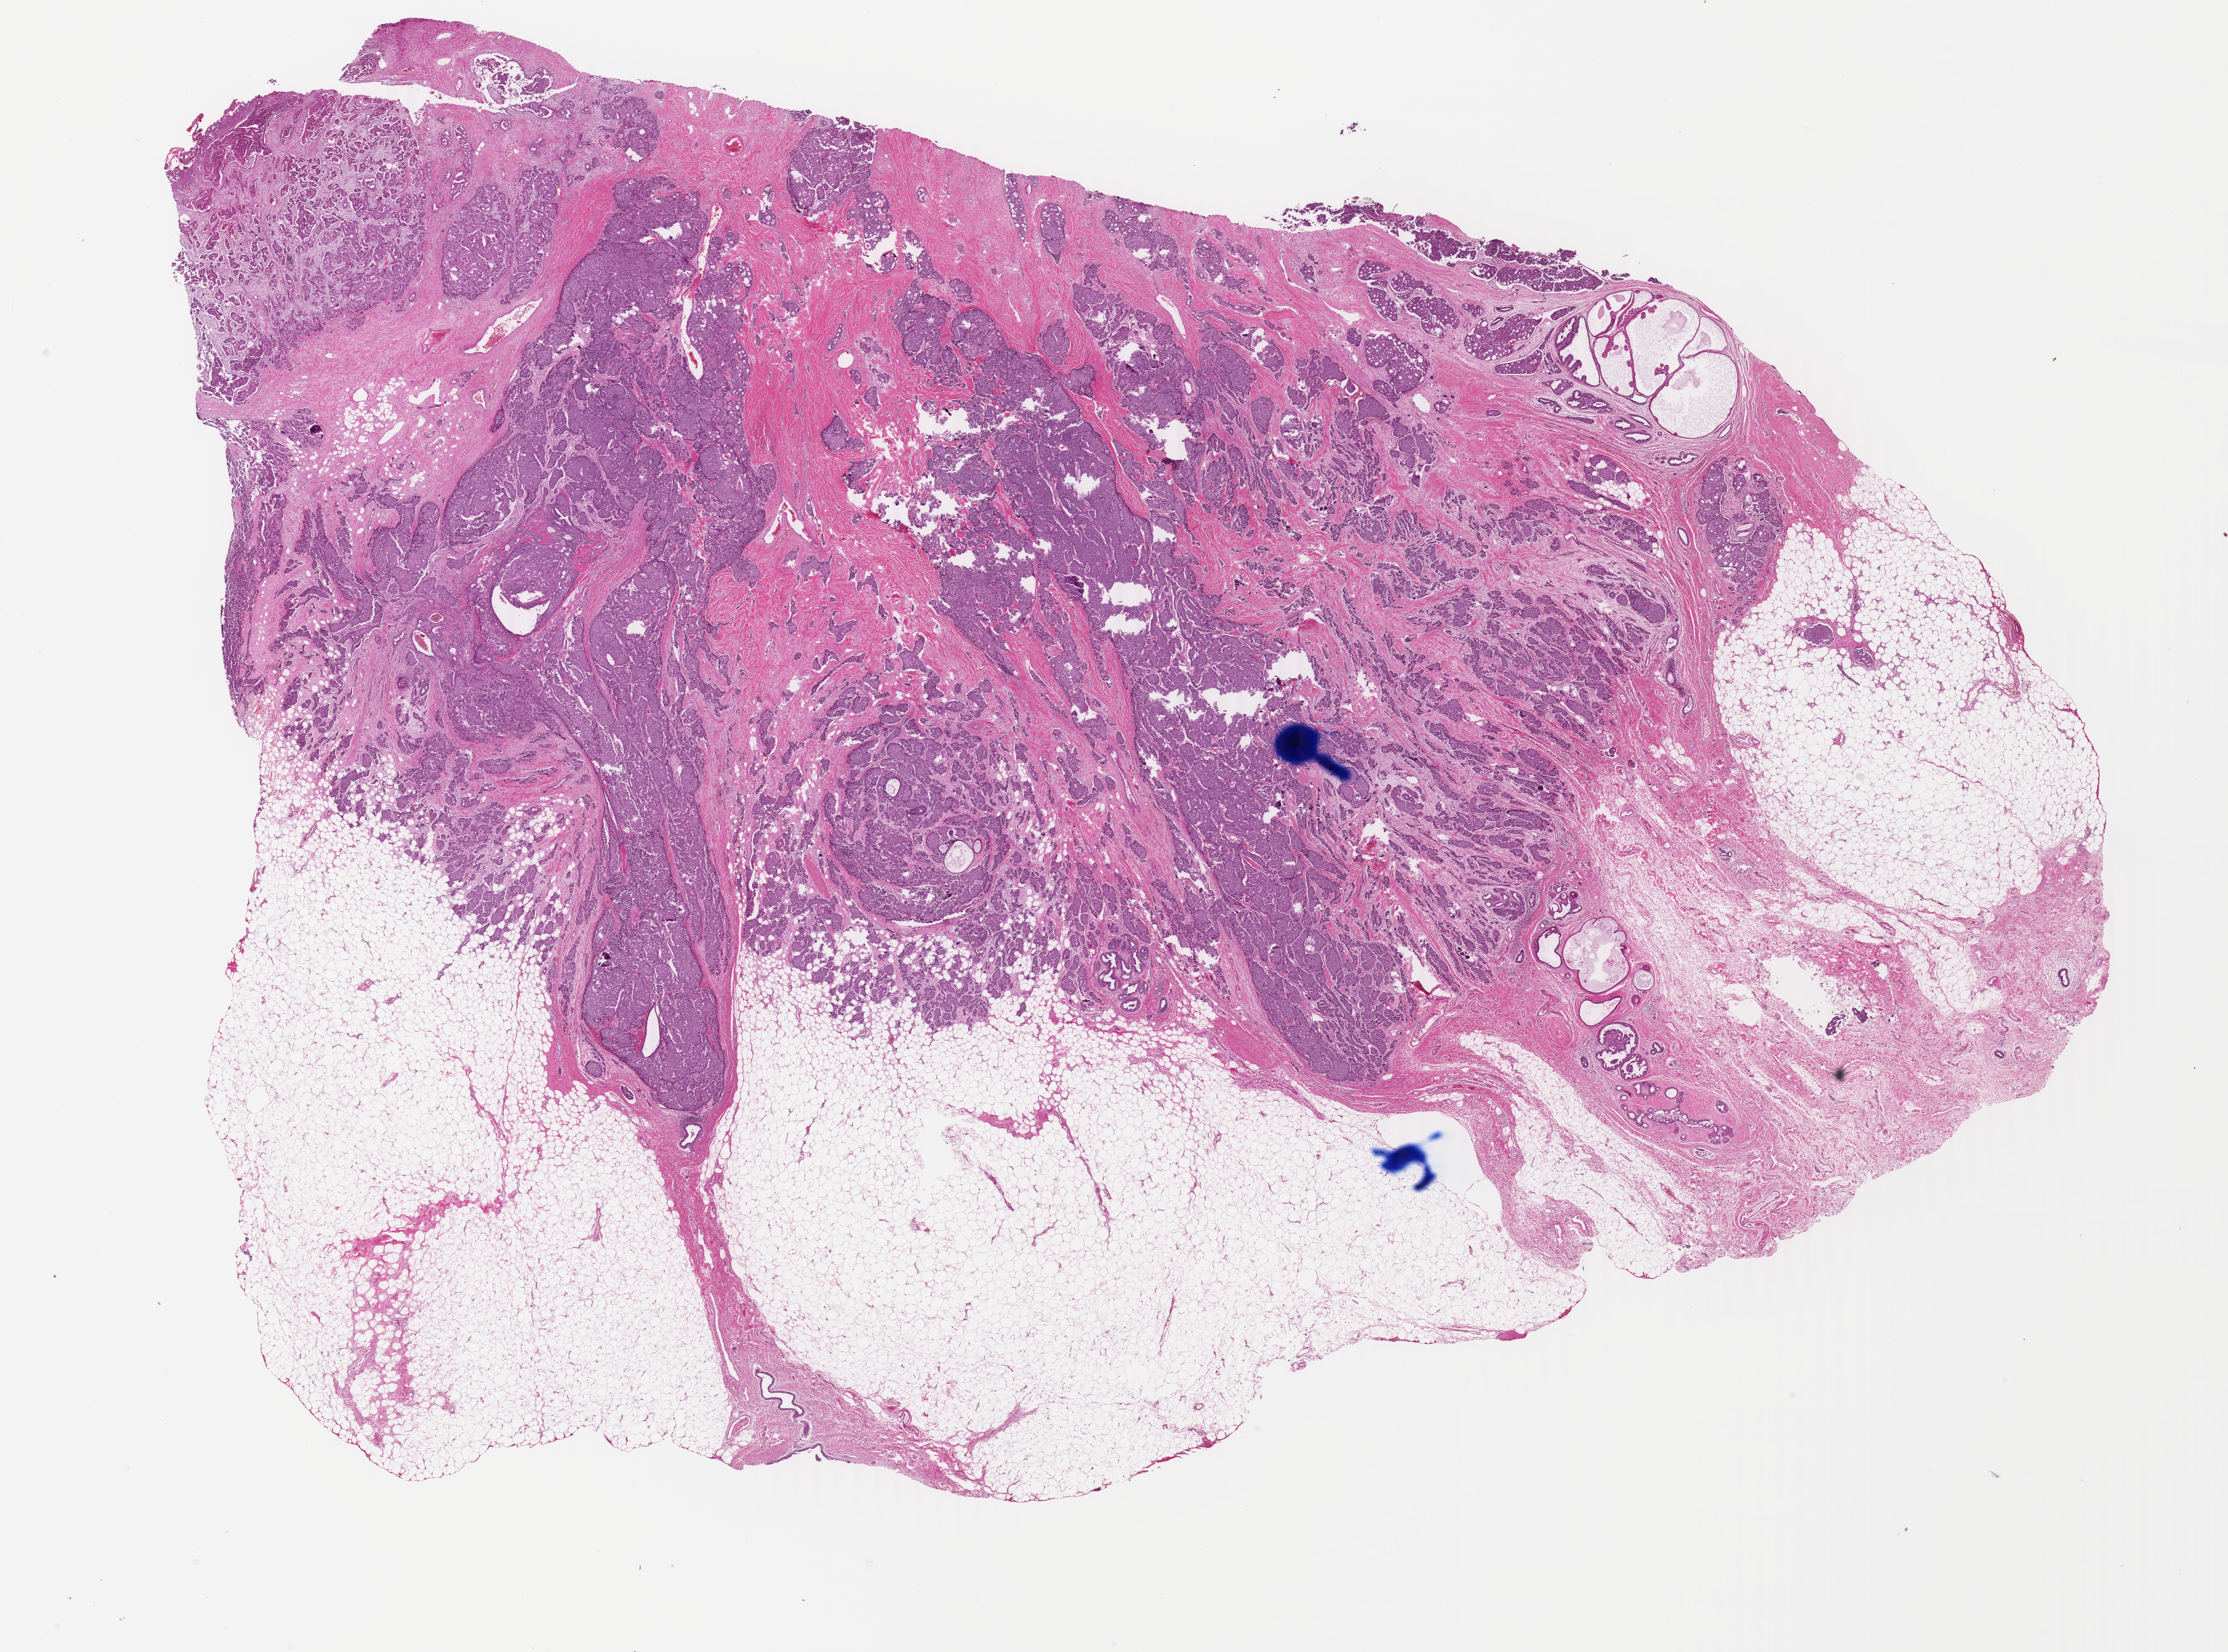
Whole-slide histology image, H&E, whole scanned area (about 26.2 x 19.4 mm) shown as a low-resolution overview. FFPE section. Breast, primary tumour sample. Female patient; age at initial diagnosis 62 years.
Diagnosis: Infiltrating duct carcinoma, NOS. Laterality: left. AJCC pathologic stage: IIB.